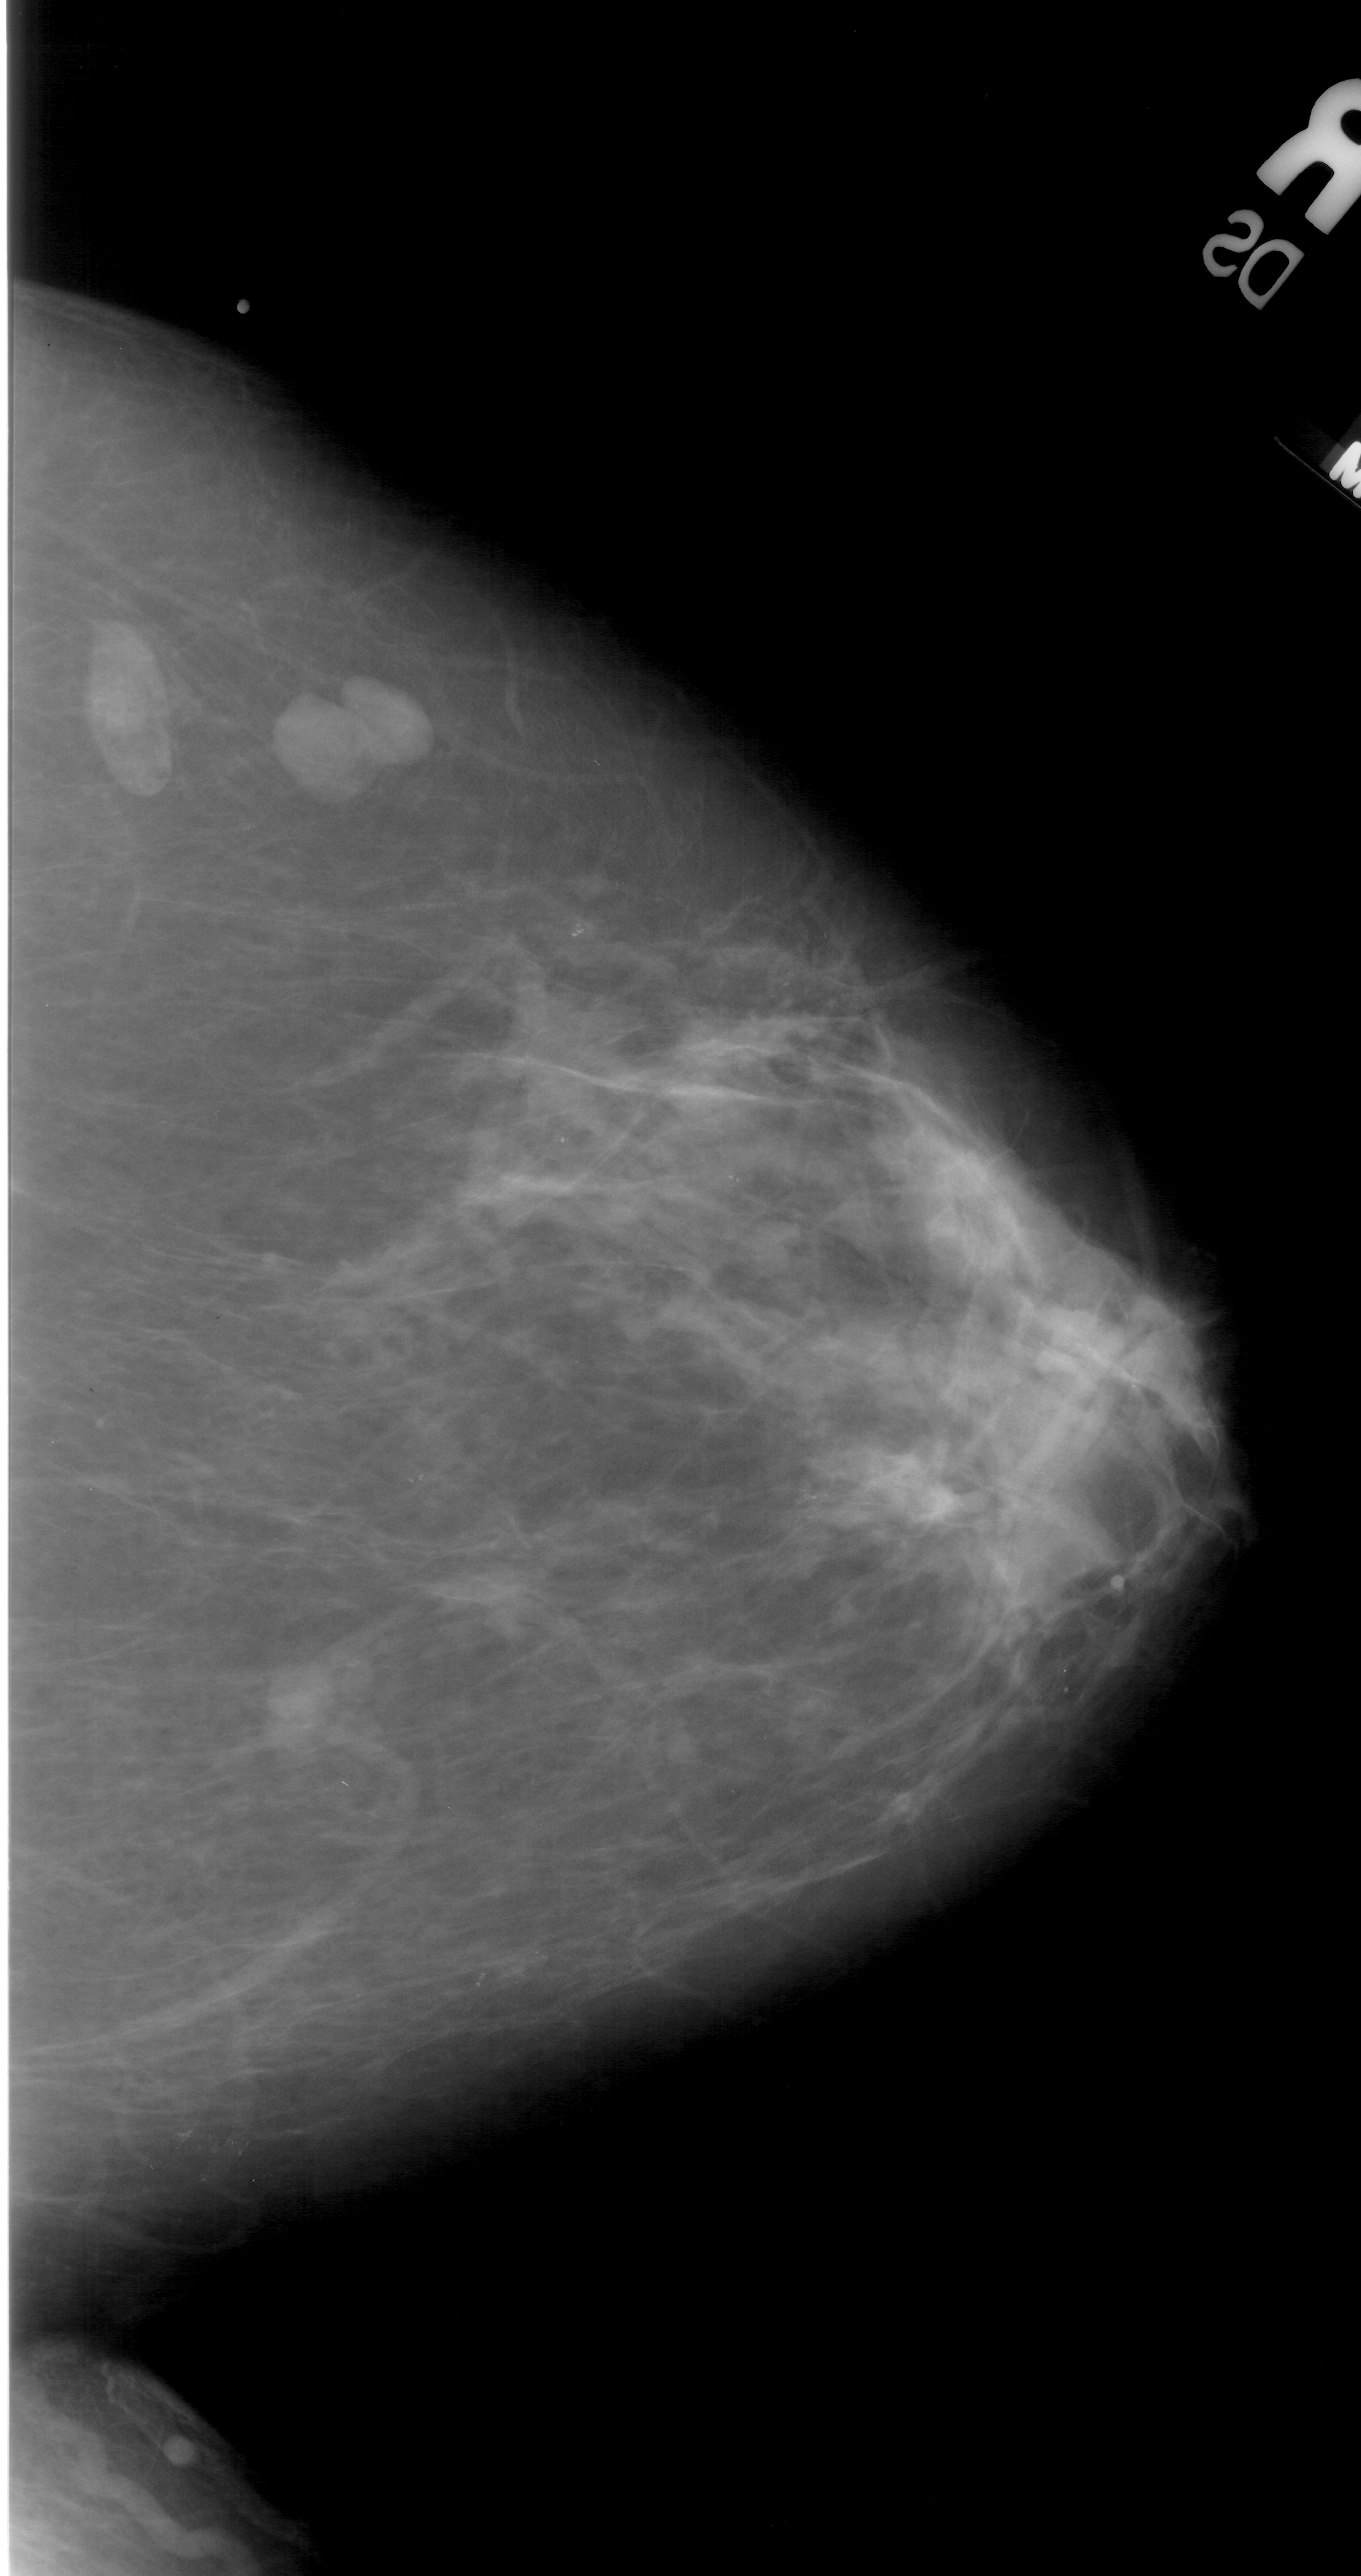
Digitized screen-film mammogram. Right breast. Craniocaudal (CC) view. Breast composition: scattered fibroglandular densities (BI-RADS density category 2 of 4). 1361 × 2576 image matrix.
Expert-marked regions of interest on this film, with their recorded descriptors:
- calcifications, morphology pleomorphic, distribution clustered; BI-RADS assessment category 3; pathology result (as recorded, not read from the image): benign: bounding box (x1, y1, x2, y2) in pixels: (698, 1141, 767, 1197)